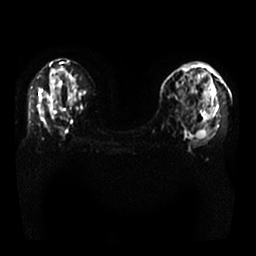
Breast MRI, one axial slice; slice 13 of 25 in the series (ordered by position); diffusion-weighted series; image 2 of 4 stored at this slice position (different b-values; order by instance number); 1.5 T; 4 mm slice thickness; 256 × 256 image matrix. Female patient.
Structures marked on this image (outlined manually by an expert reader):
- tumour on diffusion-weighted imaging: bounding box [x1, y1, x2, y2] px = [203, 87, 213, 98]